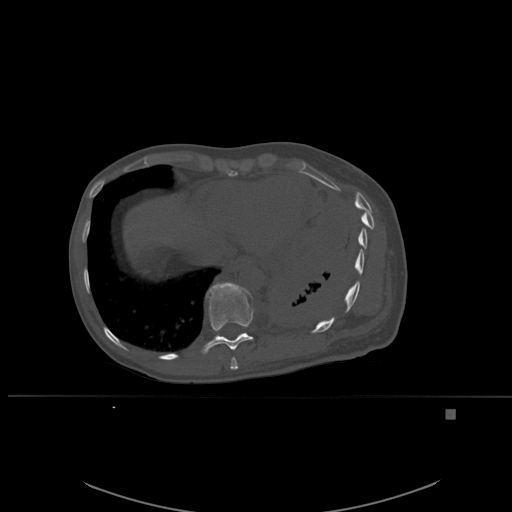
CT including the spine, one axial slice; position 317 of 537 along the scan axis; bone window (W 1800 / L 400 HU); 1.5 mm slice thickness; 512 × 512 image matrix. Patient: female, 45 years. From the clinical record (not read from this slice): primary cancer: lung.
Annotated regions visible in this slice (semi-automatically segmented with operator editing):
- T10 vertebra: box from (x=201, y=282) to (x=254, y=354) px
- T9 vertebra: (x=230, y=357)–(x=238, y=370)